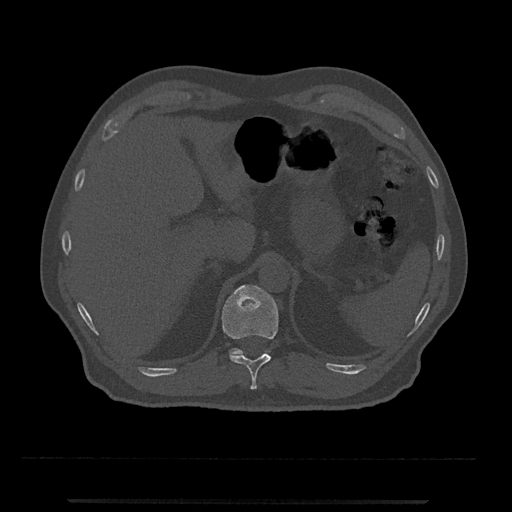
CT including the spine, one axial slice; slice 450 of 797 in the series (ordered by position); reconstruction kernel Br40s/3; bone window (W 1800 / L 400 HU); 0.5 mm slice thickness; 512 × 512 image matrix, field of view 419 × 419 mm. Patient: male, 63 years. Case-level facts recorded for this patient, not image findings: primary cancer: prostate.
Outlined on this slice (semi-automatic segmentation, software-assisted and operator-edited):
- T11 vertebra: bounding box [x1, y1, x2, y2] px = [222, 285, 278, 390]
- T12 vertebra: [229, 348, 267, 356]